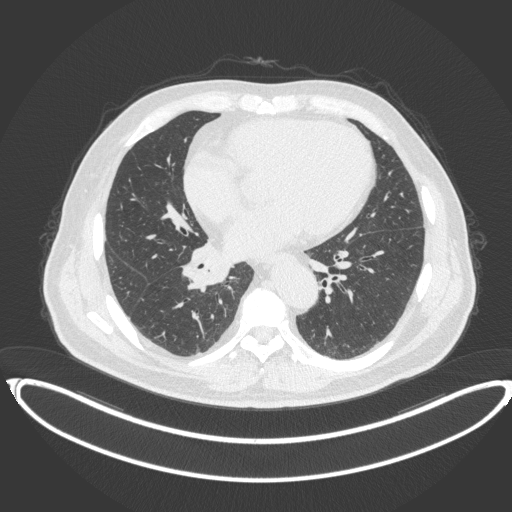
Chest CT, one axial slice. Reconstruction kernel B31f. 120 kVp. Lung window (W 1500 / L -600 HU). 1 mm slice thickness. 512 × 512 image matrix, field of view 448 × 448 mm. Male patient, age 61 years. From the clinical record (not read from this slice): clinical TNM (as recorded): T1b N1 M0.
Annotated regions visible in this slice (rectangle marked by the reading radiologist):
- lung tumour (recorded histology: squamous cell carcinoma): box from (x=177, y=240) to (x=231, y=292) px